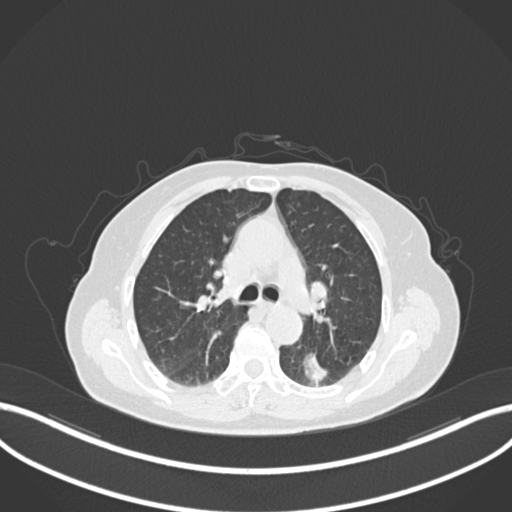
Chest CT, one axial slice; position 539 of 727 along the scan axis; reconstruction kernel B30f; 120 kVp; lung window (W 1500 / L -600 HU); 512 × 512 image matrix. Patient: female, 70 years. From the clinical record (not read from this slice): clinical TNM (as recorded): T1c N0 M0.
Annotated regions visible in this slice (bounding box drawn by a radiologist):
- lung tumour (recorded histology: adenocarcinoma): bounding box <300,351,334,389> (left, top, right, bottom; pixels)